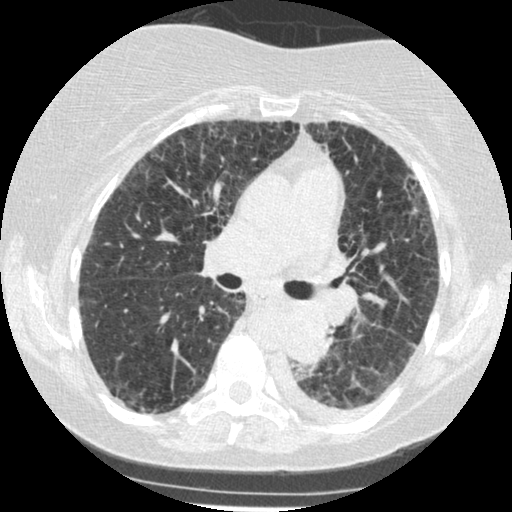
Low-dose screening chest CT, one axial slice. Slice 152 of 341 in the series (ordered by position). Reconstruction kernel STANDARD. 120 kVp. Lung window (W 1500 / L -600 HU). 512 × 512 image matrix.
Annotated regions visible in this slice (outlined manually by an expert reader):
- lesion 1 (tumor, lower lobe of left lung): box from (x=287, y=309) to (x=331, y=365) px